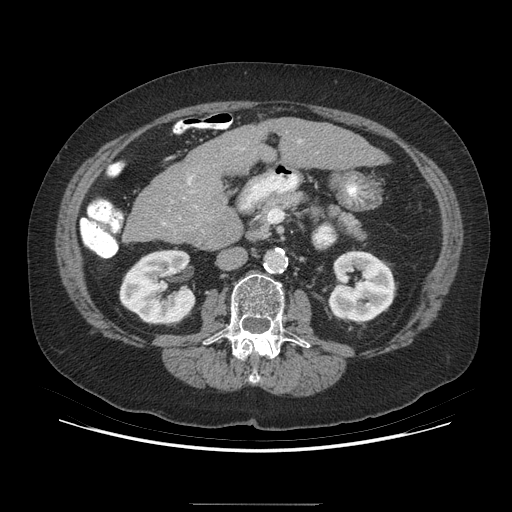
Contrast-enhanced abdominal CT (liver protocol), one axial slice; slice 137 of 192 in the series (ordered by position); reconstruction kernel STANDARD; soft-tissue window (W 400 / L 40 HU); 512 × 512 image matrix. From the clinical record (not read from this slice): diagnosis: hepatocellular carcinoma (patient treated with transarterial chemoembolisation; whether this scan precedes or follows treatment is not stated here); TNM stage (as recorded): Stage-I; Child-Pugh class: A; tumour differentiation: moderately differentiated; tumour nodularity: uninodular.
Annotated regions visible in this slice (semi-automatic segmentation, software-assisted and operator-edited):
- liver parenchyma outside the tumour (the mass and vessels are separate outlines, so this box may not span the whole liver): bounding box [x1, y1, x2, y2] px = [123, 118, 388, 246]
- mass: [225, 162, 247, 177]
- liver vessels: [164, 141, 300, 224]